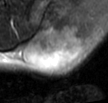
MRI of an extremity soft-tissue mass, one axial slice; position 27 of 42 along the scan axis; T2-weighted fat-saturated; MR volume resampled by the dataset authors to the PET/CT grid (not the native acquisition matrix); 108 × 103 image matrix. Male patient. Case-level facts recorded for this patient, not image findings: histological type: leiomyosarcoma; grade: intermediate; site of the primary tumour: left pelvis.
Outlined on this slice (expert contour drawn on MRI and transferred to this co-registered scan by the dataset authors):
- gross tumour volume (mass): bounding box [x1, y1, x2, y2] px = [23, 23, 84, 72]